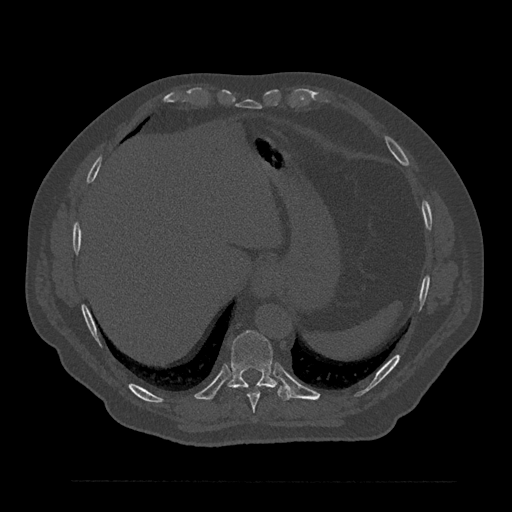
CT including the spine, one axial slice. Position 373 of 797 along the scan axis. Reconstruction kernel Br40s/3. 120 kVp. Bone window (W 1800 / L 400 HU). 0.5 mm slice thickness. 512 × 512 image matrix, field of view 430 × 430 mm. Patient: male, 61 years. From the clinical record (not read from this slice): primary cancer: prostate.
Structures marked on this image (semi-automatic segmentation, software-assisted and operator-edited):
- T10 vertebra: bounding box (x1, y1, x2, y2) in pixels: (228, 331, 292, 401)
- T9 vertebra: (242, 384, 267, 413)